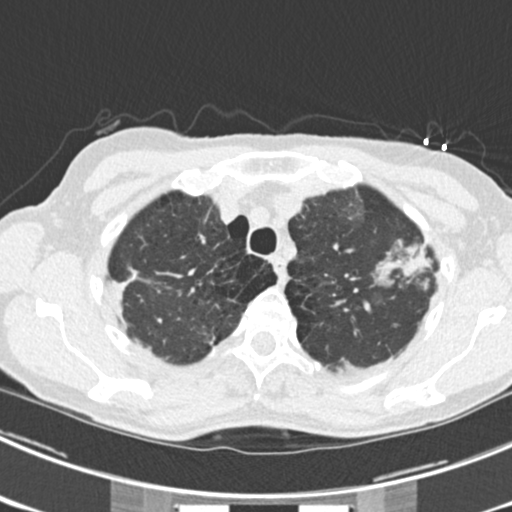
Low-dose screening chest CT, one axial slice; position 181 of 225 along the scan axis; lung window (W 1500 / L -600 HU); 2 mm slice thickness; 512 × 512 image matrix, field of view 302 × 302 mm.
Outlined on this slice (outlined manually by an expert reader):
- lesion 1 (tumor, upper lobe of left lung): bounding box (x1, y1, x2, y2) in pixels: (374, 242, 432, 286)